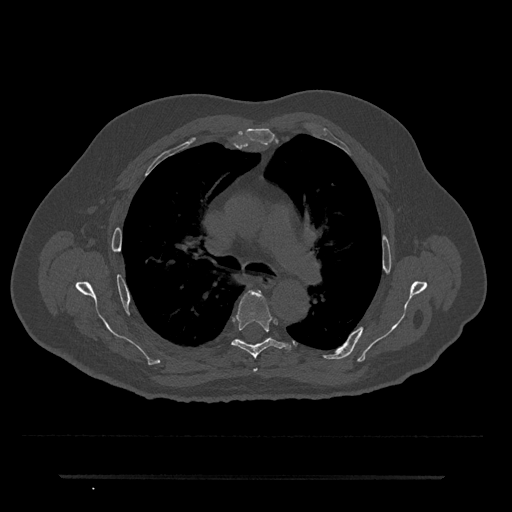
CT including the spine, one axial slice. Slice 483 of 797 in the series (ordered by position). Reconstruction kernel Br40s/3. 120 kVp. Bone window (W 1800 / L 400 HU). 0.5 mm slice thickness. 512 × 512 image matrix. Patient: male, 69 years. From the clinical record (not read from this slice): primary cancer: prostate.
Structures marked on this image (semi-automatically segmented with operator editing):
- T4 vertebra: bounding box [x1, y1, x2, y2] px = [254, 369, 257, 371]
- T5 vertebra: [231, 290, 292, 358]